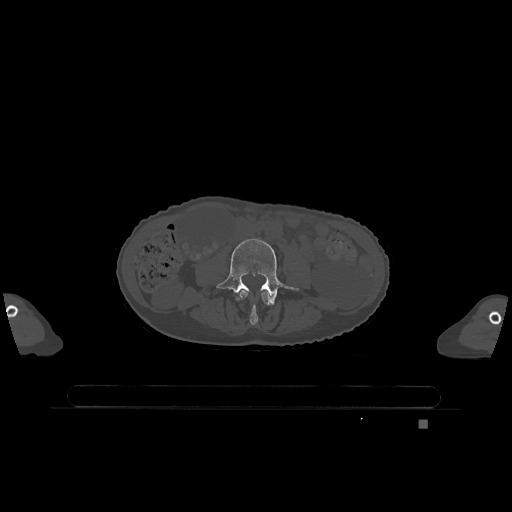
CT including the spine, one axial slice; slice 311 of 1317 in the series (ordered by position); bone window (W 1800 / L 400 HU); 512 × 512 image matrix, field of view 500 × 500 mm. Female patient, age 74 years. Case-level facts recorded for this patient, not image findings: primary cancer: lung.
Annotated regions visible in this slice (semi-automatically segmented with operator editing):
- L3 vertebra: box from (x=239, y=290) to (x=271, y=325) px
- L4 vertebra: (x=216, y=238)–(x=299, y=305)